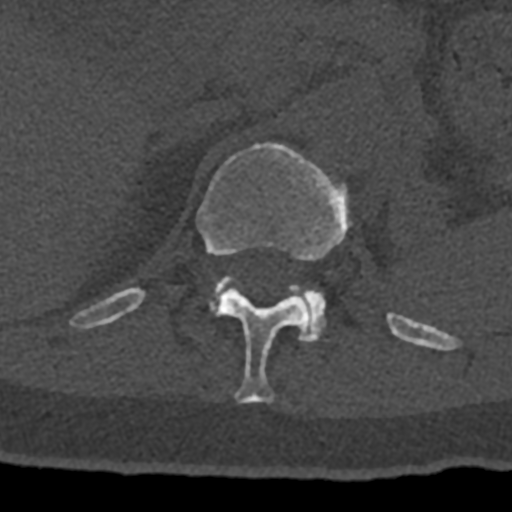
CT including the spine, one axial slice. Position 479 of 797 along the scan axis. Reconstruction kernel Br40s/3. 120 kVp. Bone window (W 1800 / L 400 HU). 0.5 mm slice thickness. 512 × 512 image matrix, field of view 160 × 160 mm. Male patient, age 74 years. Case-level facts recorded for this patient, not image findings: primary cancer: renal.
Annotated regions visible in this slice (semi-automatically segmented with operator editing):
- L1 vertebra: bounding box [x1, y1, x2, y2] px = [210, 276, 325, 342]
- T12 vertebra: [71, 142, 432, 403]